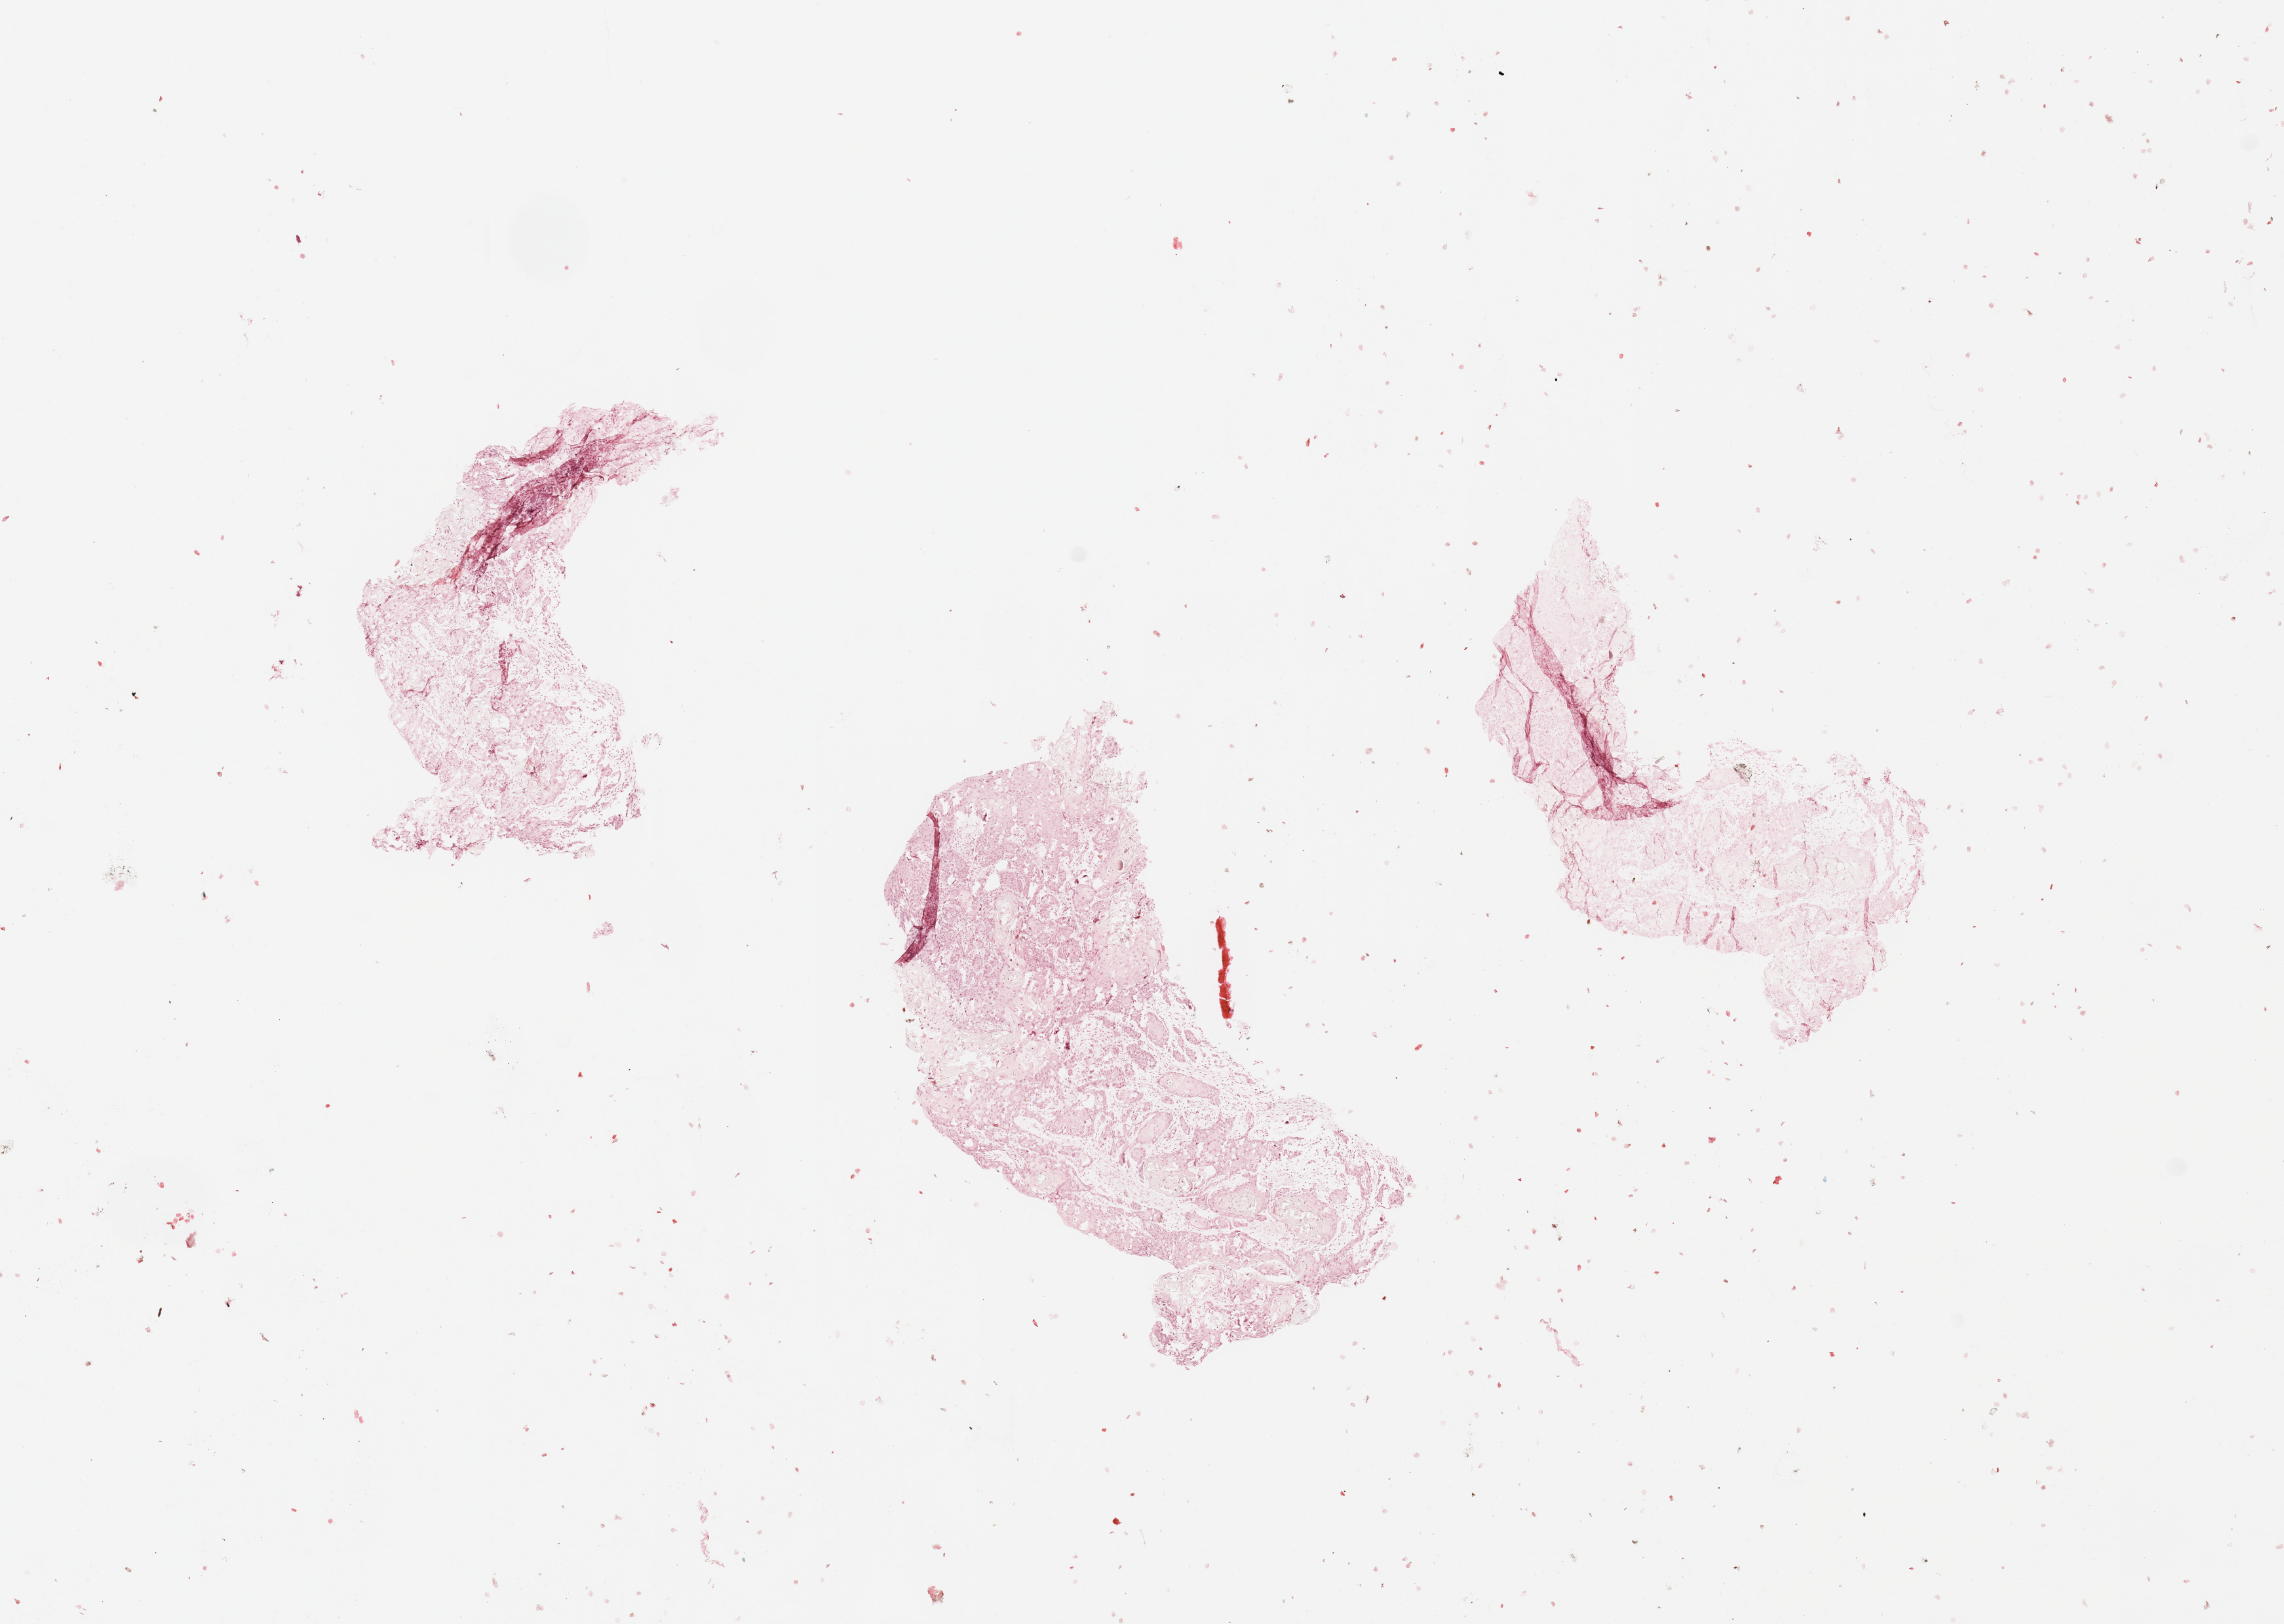
Digitized H&E-stained tissue section (whole slide), shown as a low-resolution overview of the whole scanned area (about 13.8 x 9.8 mm), tumour tissue sample, sampled site: tongue. Male, 64 y/o. Histologic grade: G2 (moderately differentiated). Pathologist review of this section (percent, as recorded): tumour nuclei 80%, necrosis 0%.
Diagnosis: Squamous cell carcinoma, NOS (tongue, NOS). AJCC pathologic stage: III.